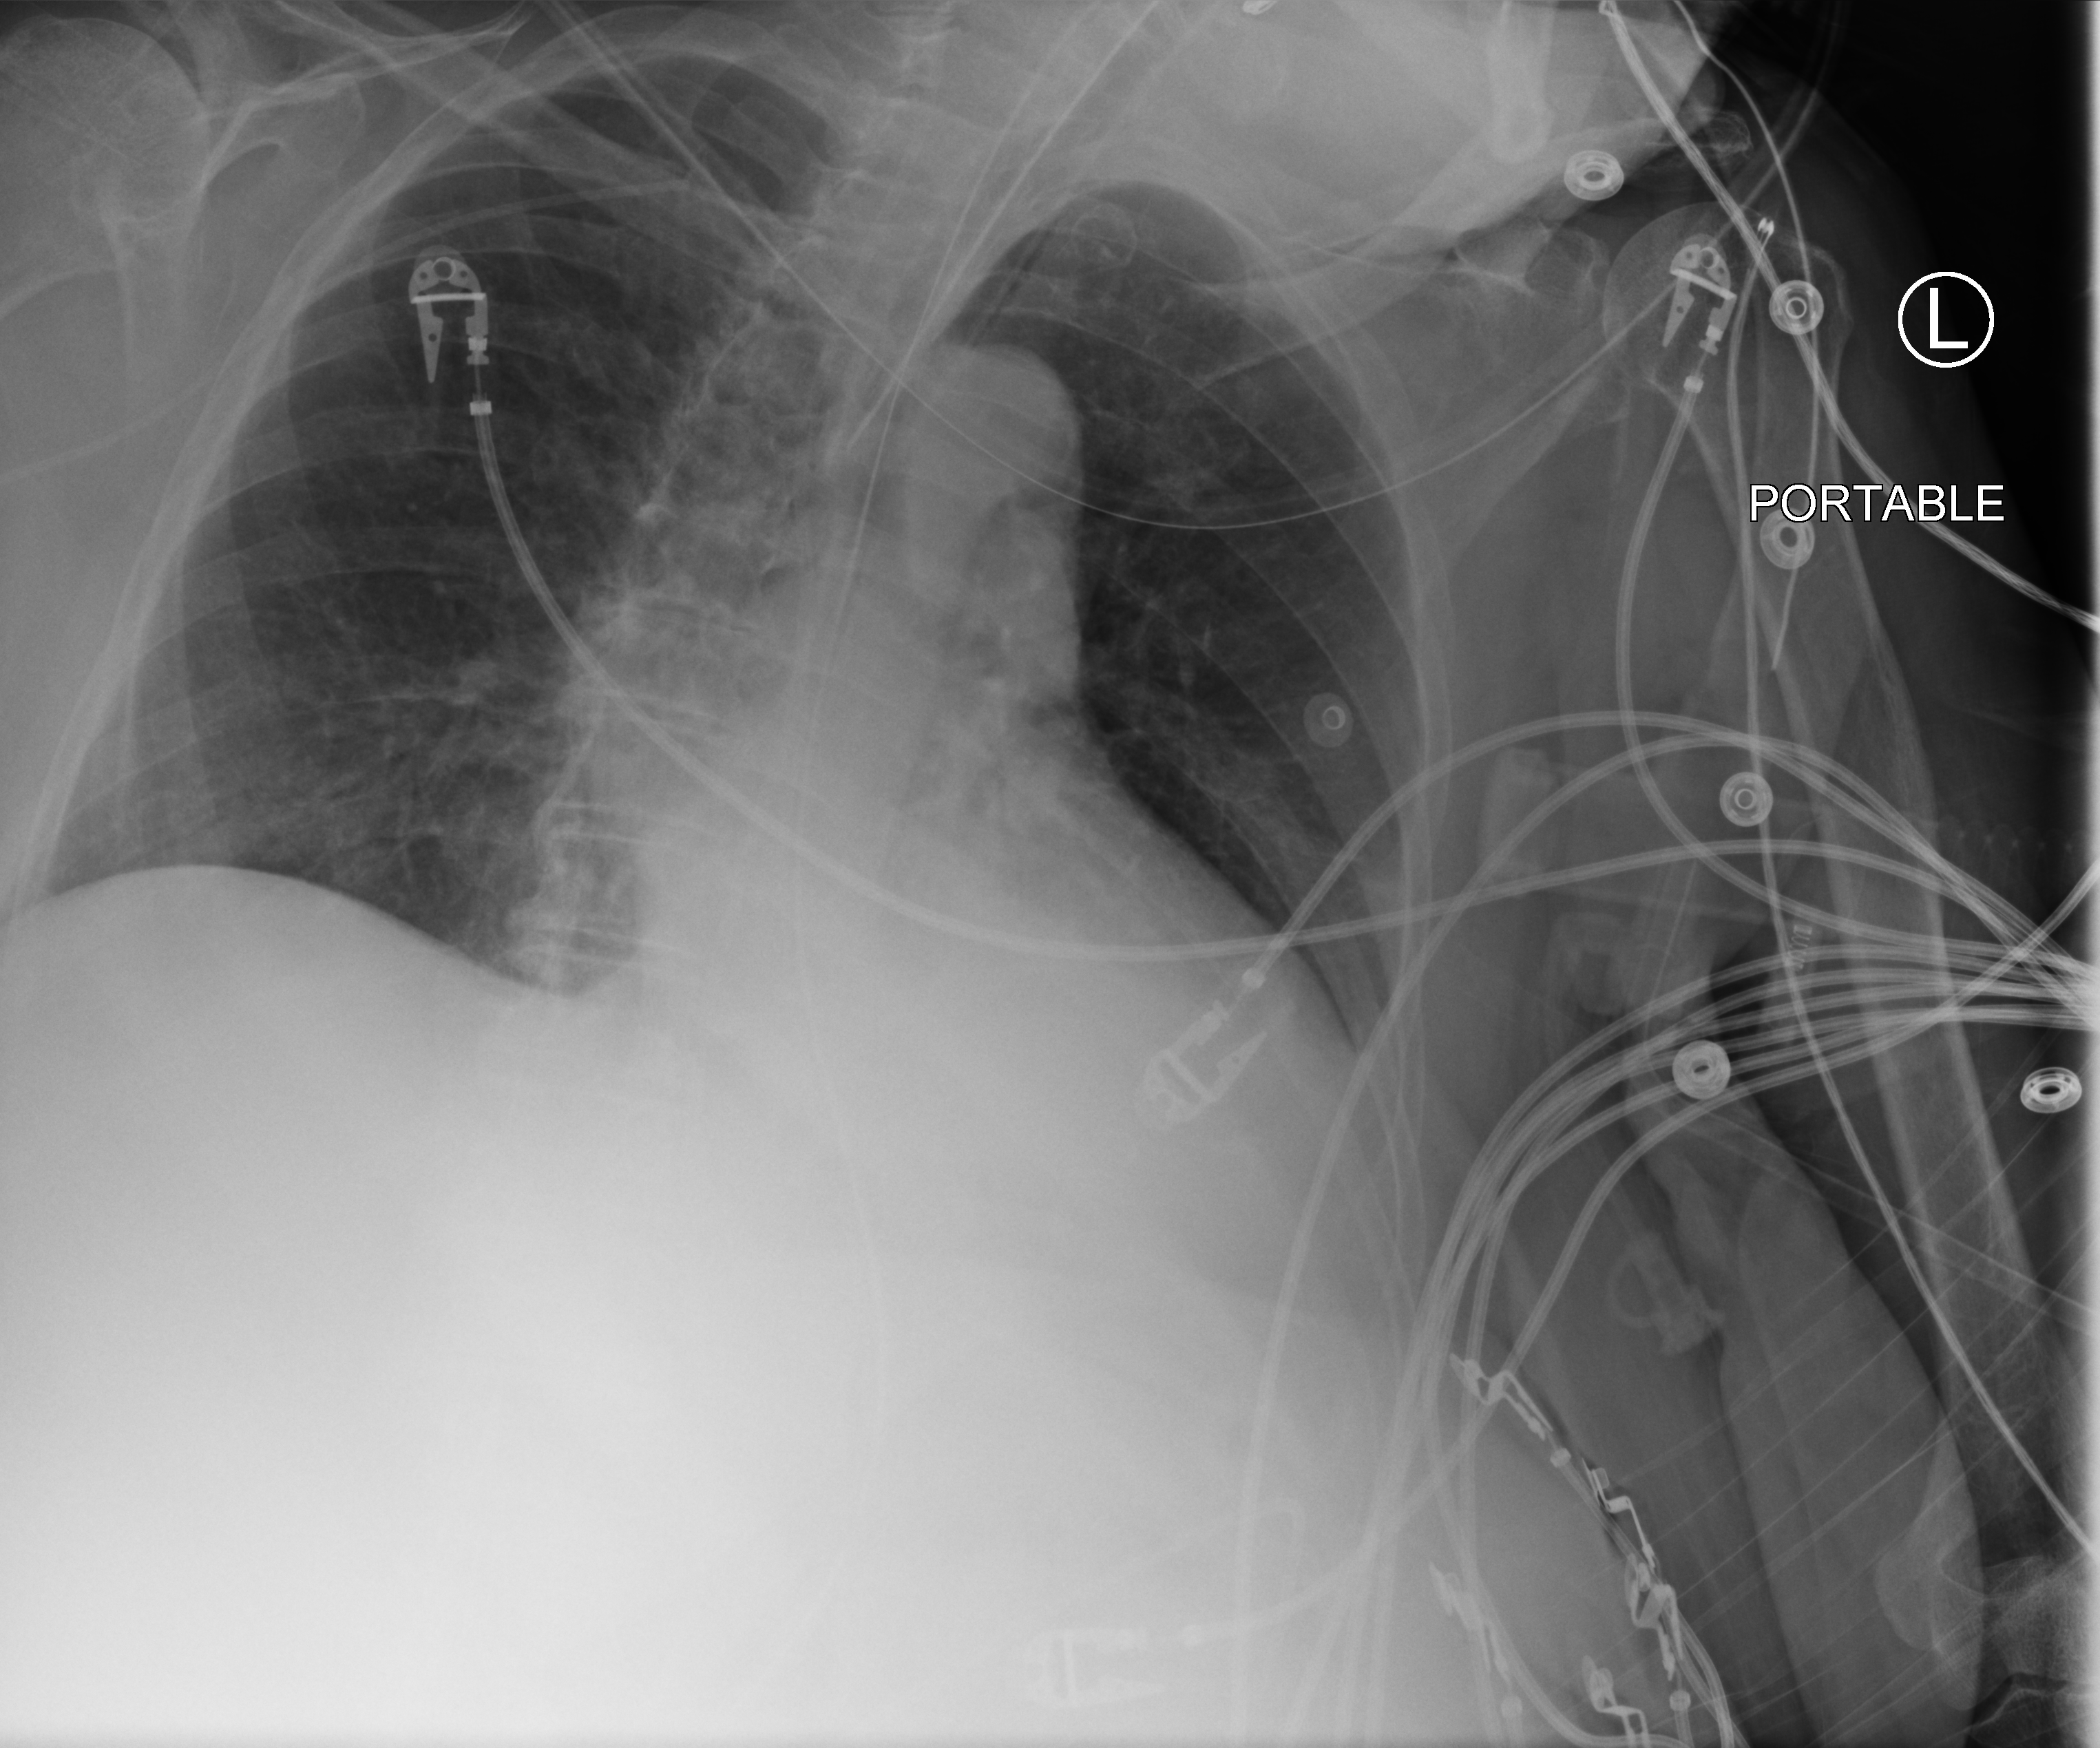
Chest X-ray (portable), anteroposterior (AP) projection. Patient hospitalised with COVID-19; female, aged 75–90 years.
From the hospital-stay record, not from the radiograph (when in the stay this image was taken is not recorded): other chronic lung disease (admission record): no.